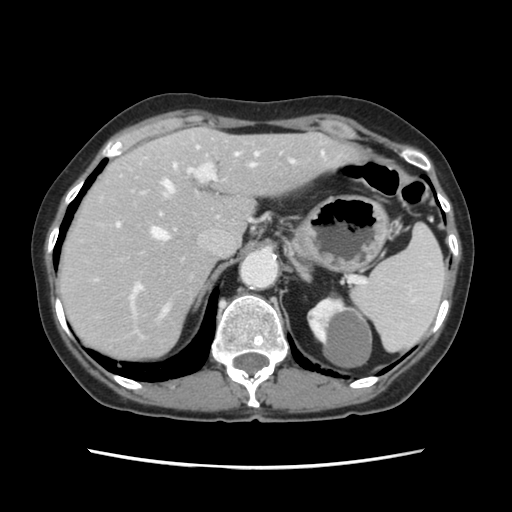
Contrast-enhanced abdominal CT, one axial slice. Position 88 of 120 along the scan axis. 120 kVp. Intravenous contrast given. Soft-tissue window (W 400 / L 40 HU). 2.5 mm slice thickness. 512 × 512 image matrix, field of view 330 × 330 mm. Female patient, age 70 years. From the clinical record (not read from this slice): diagnosis: colorectal cancer liver metastases, imaged before liver resection.
Outlined on this slice (manually delineated by an expert):
- hepatic veins: box from (x=151, y=153) to (x=255, y=319) px
- liver: (x=60, y=128)–(x=351, y=359)
- planned liver remnant (the part of the liver to remain after resection): (x=116, y=129)–(x=351, y=290)
- portal vein (with intrahepatic branches): (x=116, y=146)–(x=295, y=308)